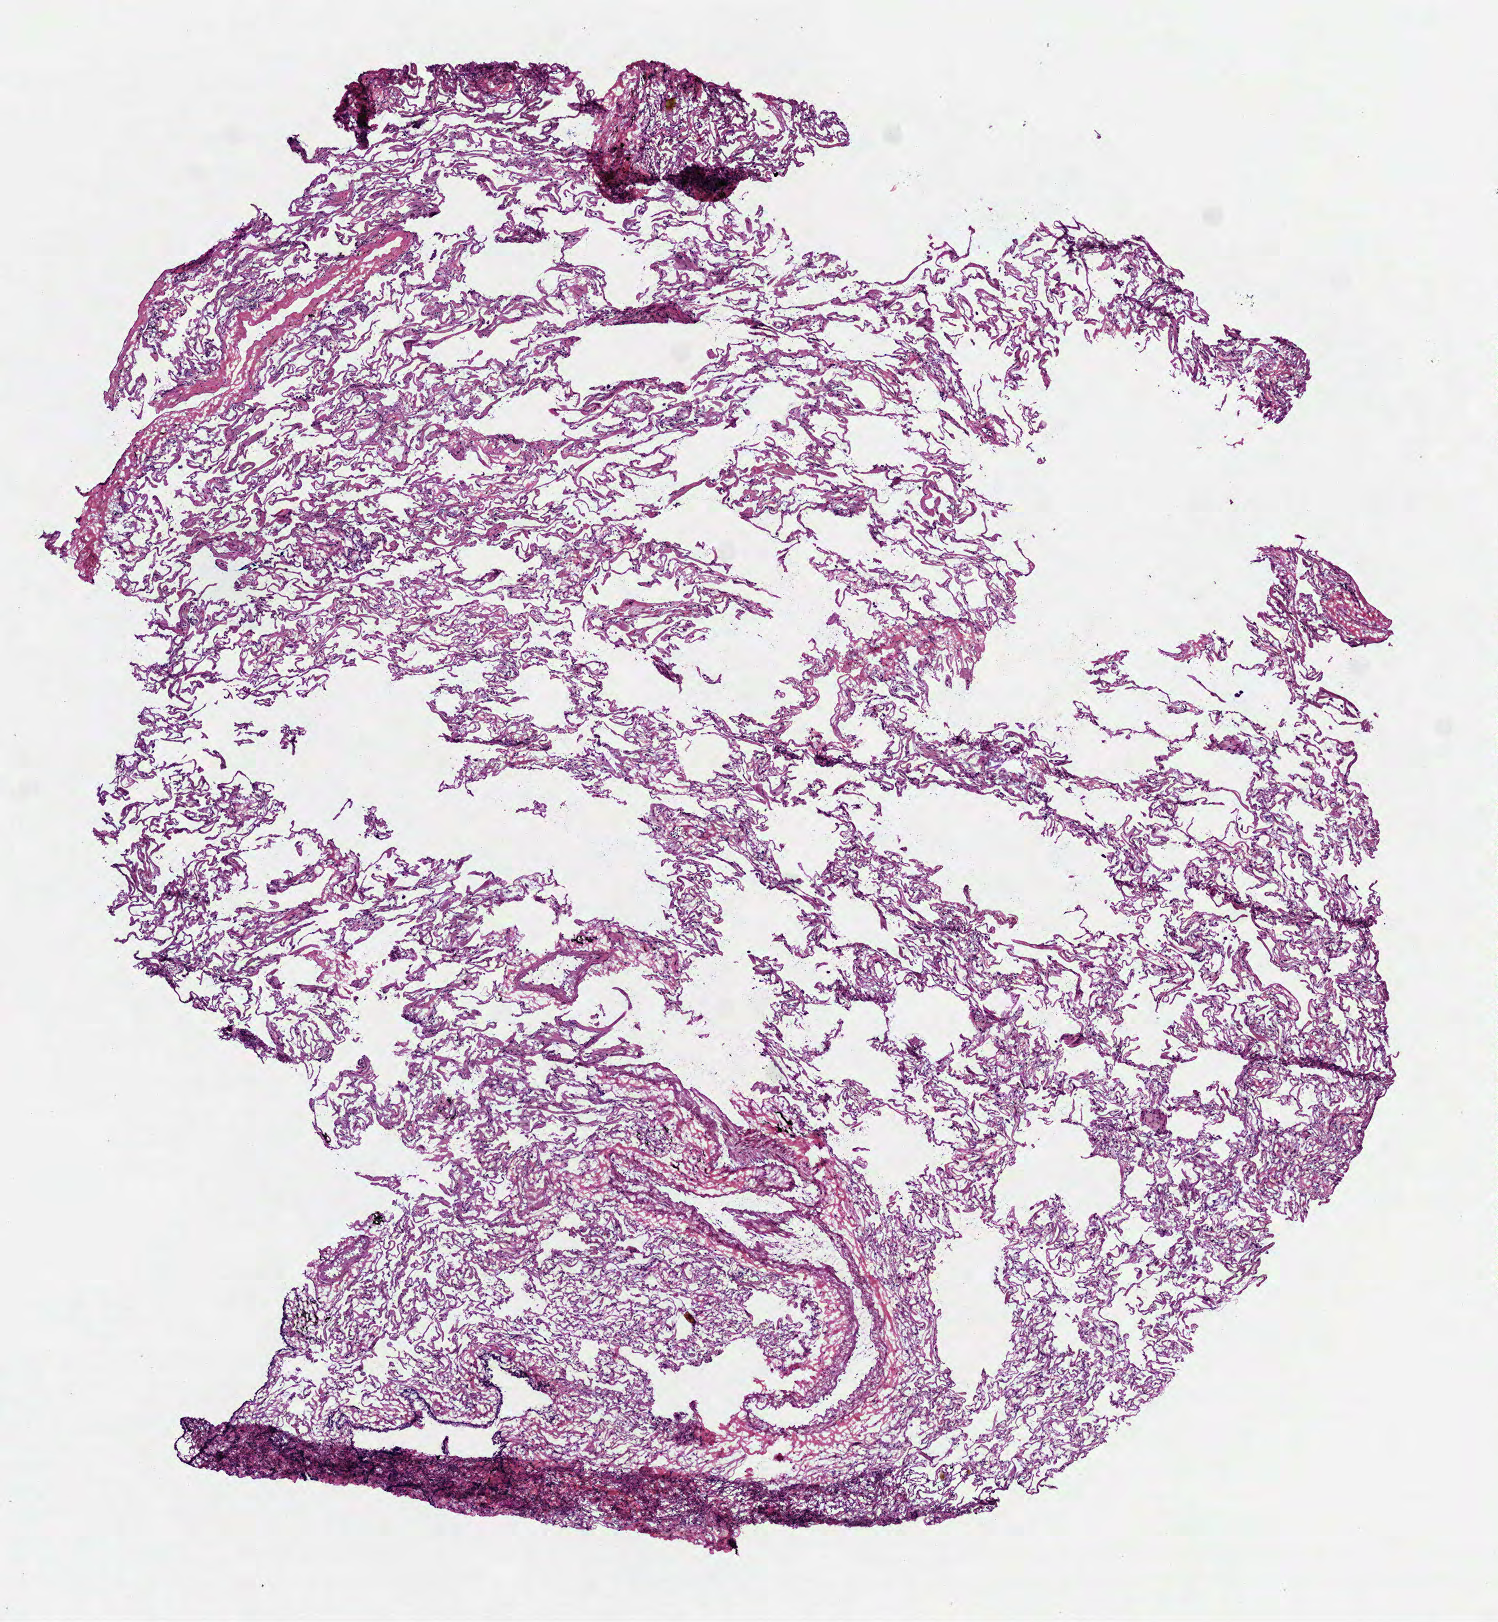
H&E whole-slide image — whole scanned area (about 6.0 x 6.5 mm) shown as a low-resolution overview; frozen section from the top of the tissue portion; sample: solid tissue normal (non-tumour tissue), lung. Patient: female, age at initial diagnosis 72 years.
- this section: solid tissue normal sample (biorepository sample class)
- patient diagnosis: Adenocarcinoma, NOS (upper lobe, lung)